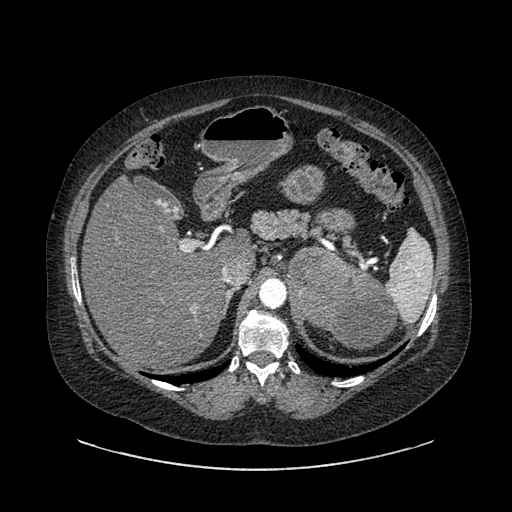
Contrast-enhanced abdominal CT, one axial slice. Slice 597 of 769 in the series (ordered by position). 120 kVp. Soft-tissue window (W 400 / L 40 HU). 0.62 mm slice thickness. 512 × 512 image matrix, field of view 460 × 460 mm. Patient: female, 61 years. Case-level facts recorded for this patient, not image findings: diagnosis: adrenocortical carcinoma; tumour side: left adrenal; tumour size at pathology: 13 cm; Ki-67 index: 79 %.
Annotated regions visible in this slice (semi-automatic segmentation, software-assisted and operator-edited):
- mass: bounding box (x1, y1, x2, y2) in pixels: (288, 249, 394, 348)